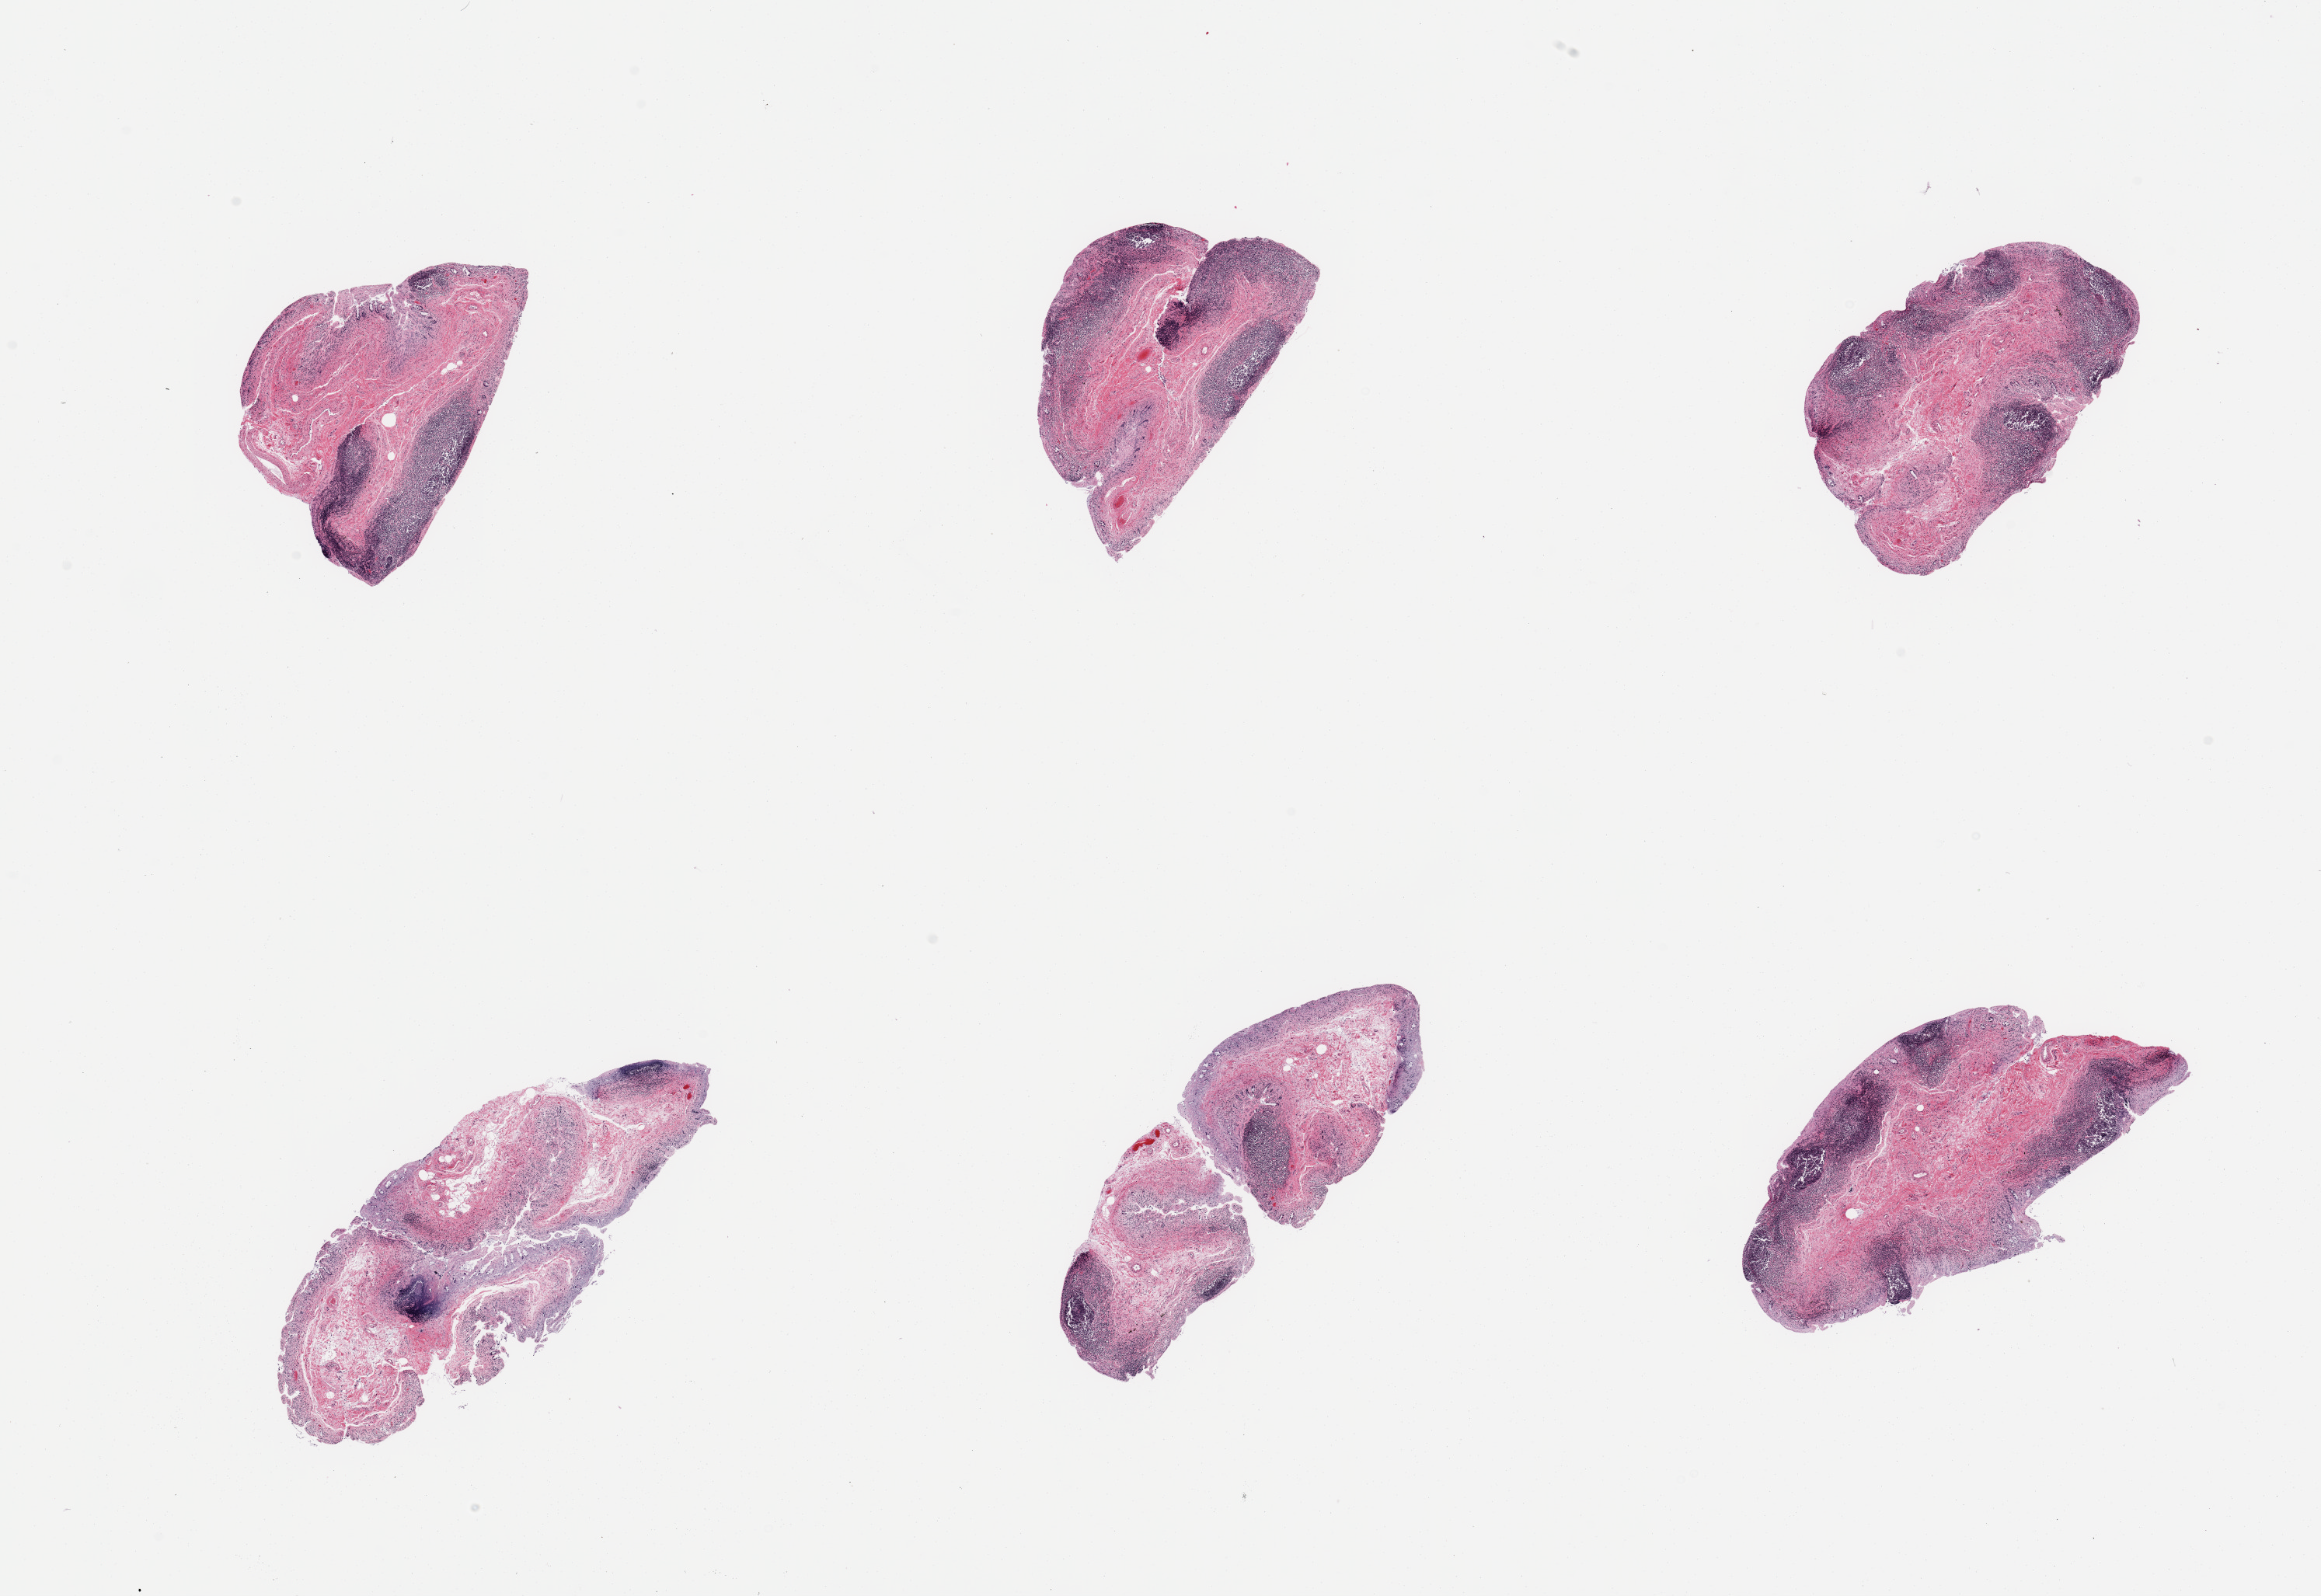
Digitized H&E-stained section — a low-resolution overview of the entire scanned area, about 23.6 x 16.2 mm. PAXgene-fixed paraffin-embedded (PFPE) section. Target tissue: ileum. Donor tissue sample. Donor: male.
Reviewer comment on this tissue sample: 6 pieces; autolyzed mucosa but residual target lymphoid aggregates represent at least 30% of tissue.